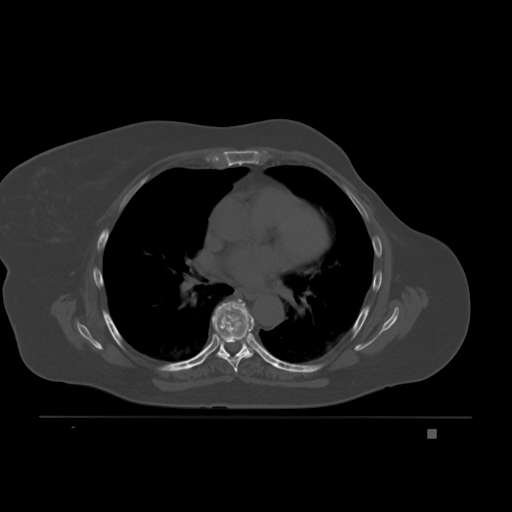
CT including the spine, one axial slice; slice 132 of 221 in the series (ordered by position); bone window (W 1800 / L 400 HU); 3 mm slice thickness; 512 × 512 image matrix, field of view 474 × 474 mm. Female patient, age 63 years. From the clinical record (not read from this slice): primary cancer: breast.
Structures marked on this image (semi-automatic segmentation, software-assisted and operator-edited):
- T6 vertebra: bounding box (x1, y1, x2, y2) in pixels: (216, 354, 252, 373)
- T7 vertebra: (212, 299, 254, 356)